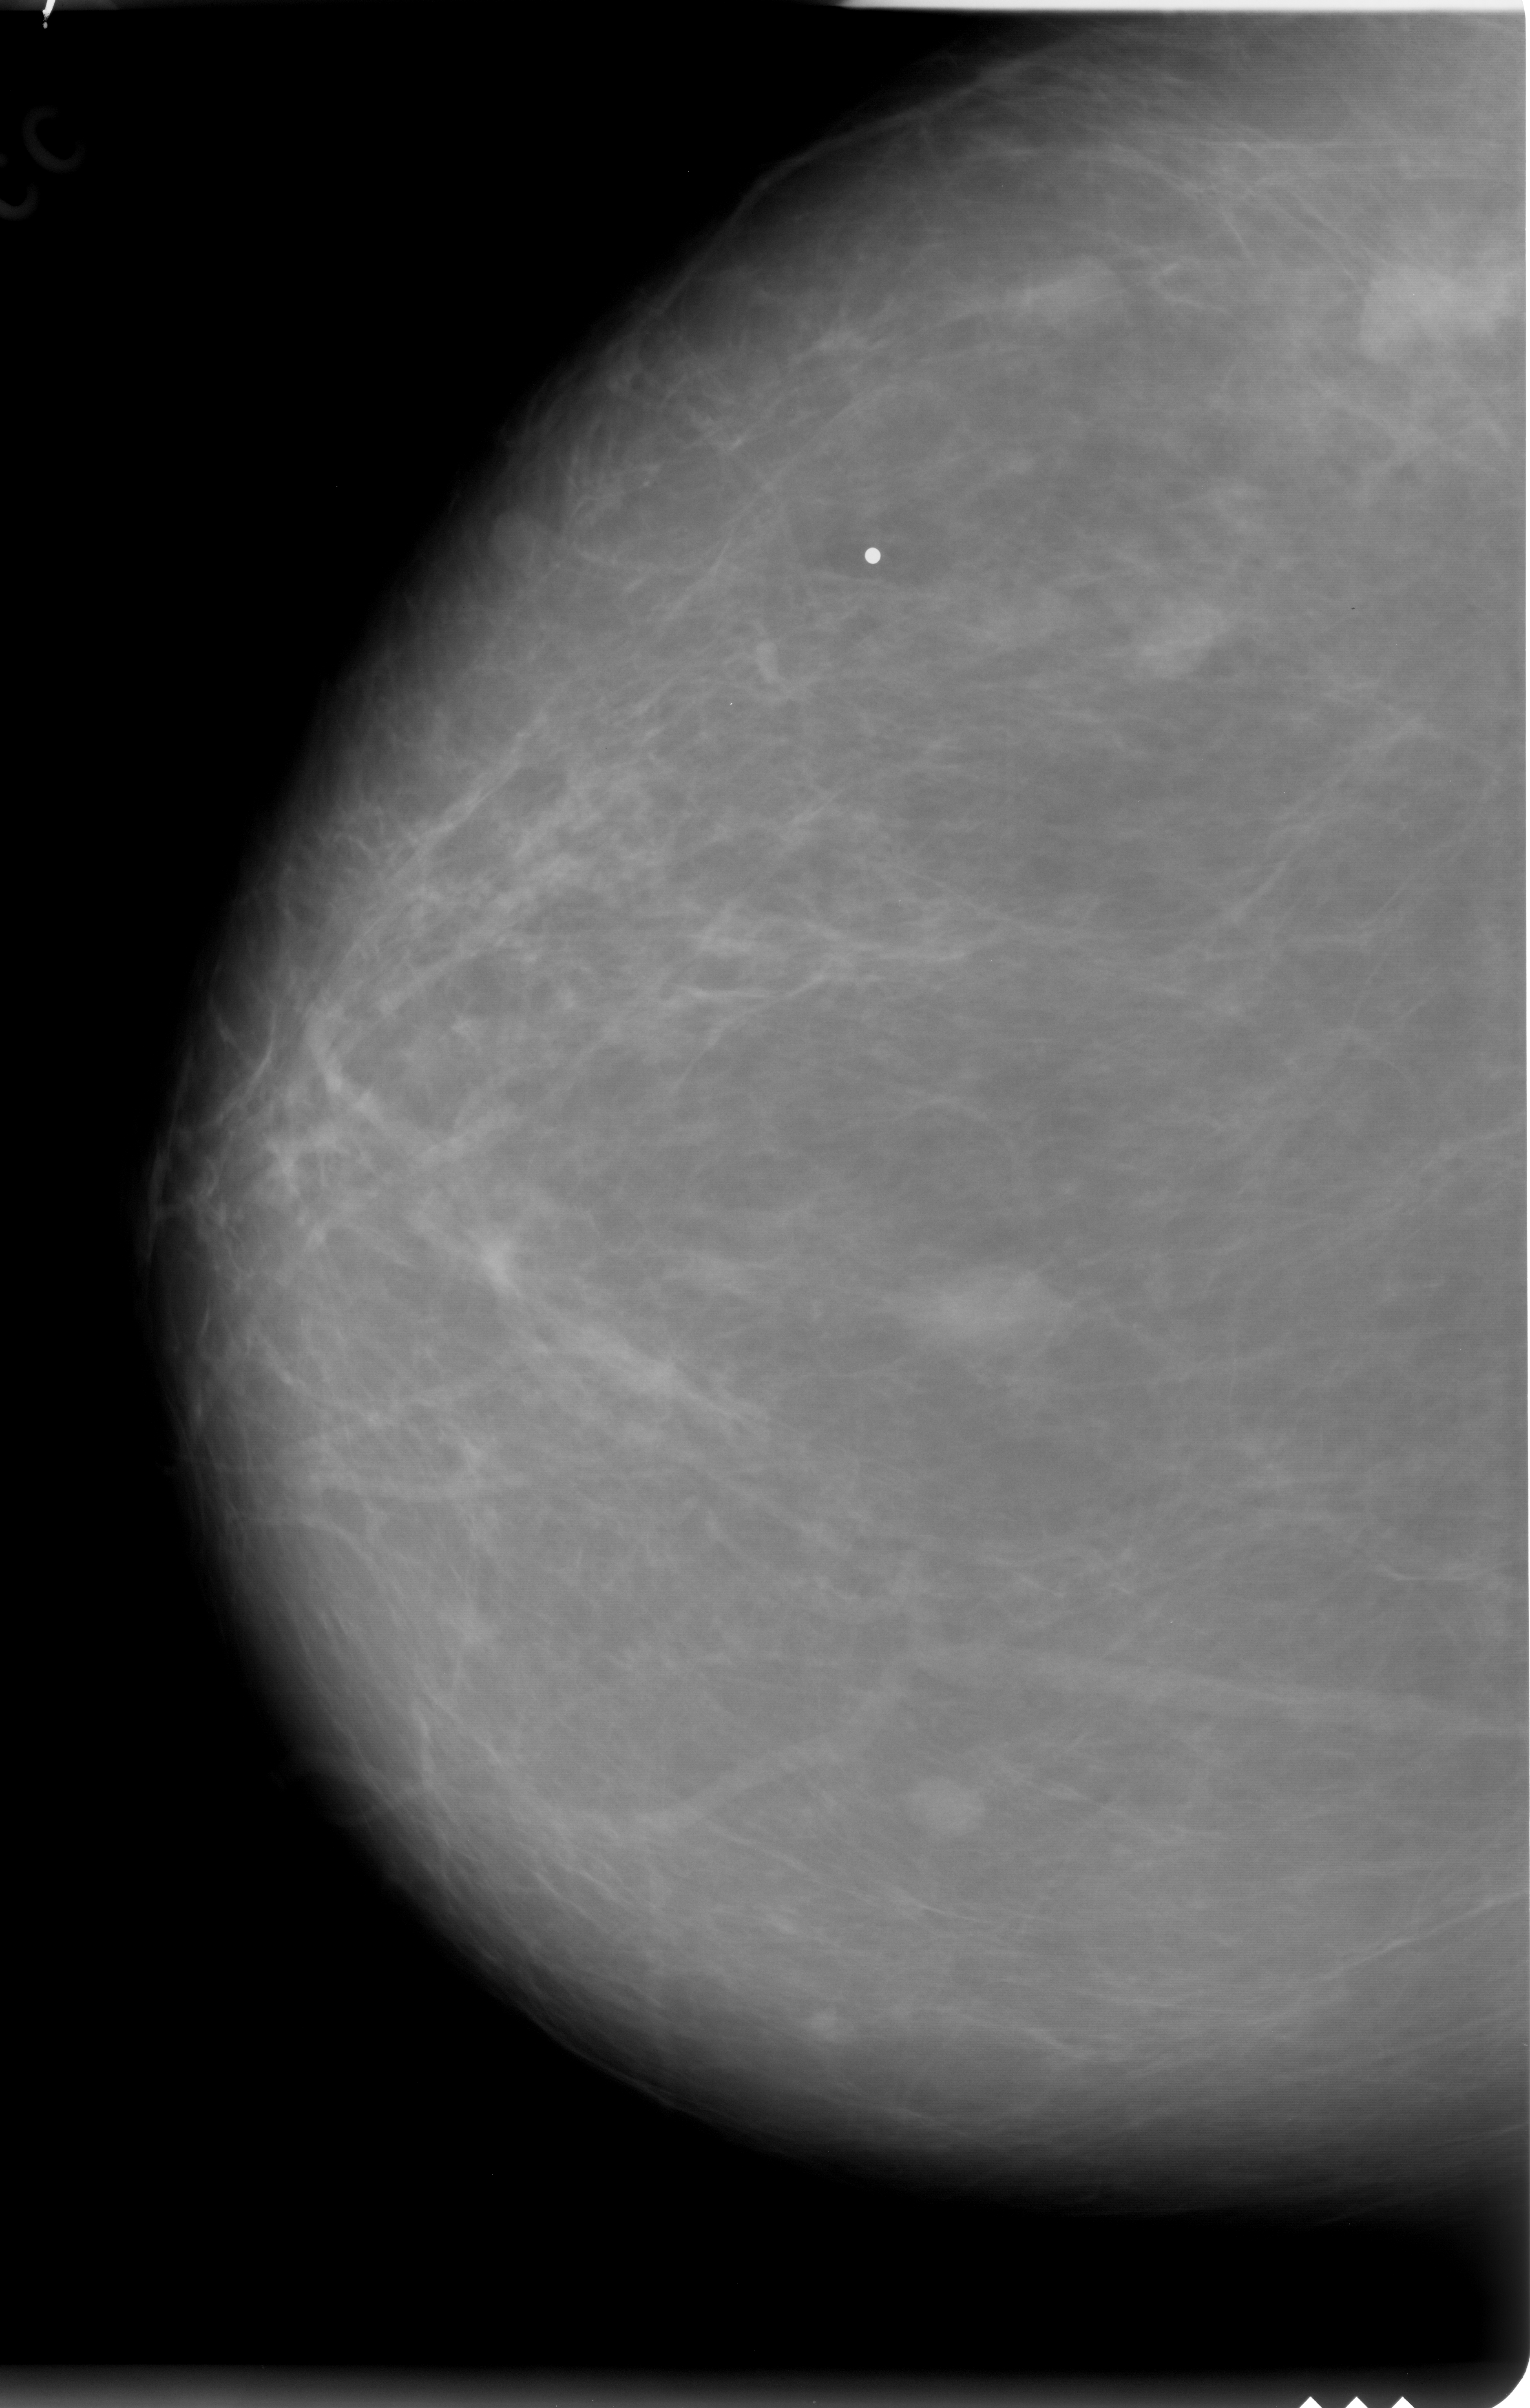
Scanned film-screen mammogram; right breast; craniocaudal (CC) view; breast composition: almost entirely fatty (BI-RADS density category 1 of 4); 1530 × 2408 image matrix.
Expert-marked regions of interest on this film, with their recorded descriptors:
- Finding 1 of 5: mass, shape round, margins circumscribed; BI-RADS assessment category 2; pathology (as recorded): benign: bounding box [x1, y1, x2, y2] px = [482, 500, 569, 587]
- Finding 2 of 5: mass, shape round, margins circumscribed; BI-RADS assessment category 2; subtlety rating 5 on a 1 (subtle) to 5 (obvious) scale; pathology result (as recorded, not read from the image): benign: [897, 1766, 998, 1870]
- Finding 3 of 5: mass, shape round, margins circumscribed; BI-RADS assessment category 2; pathology (as recorded): benign: [999, 253, 1124, 340]
- Finding 4 of 5: mass, shape round, margins circumscribed; BI-RADS assessment category 2; subtlety rating 5 on a 1 (subtle) to 5 (obvious) scale; pathology result (as recorded, not read from the image): benign: [1117, 595, 1232, 687]
- Finding 5 of 5: mass, shape round, margins circumscribed; BI-RADS assessment category 2; pathology (as recorded): benign: [1369, 253, 1497, 353]